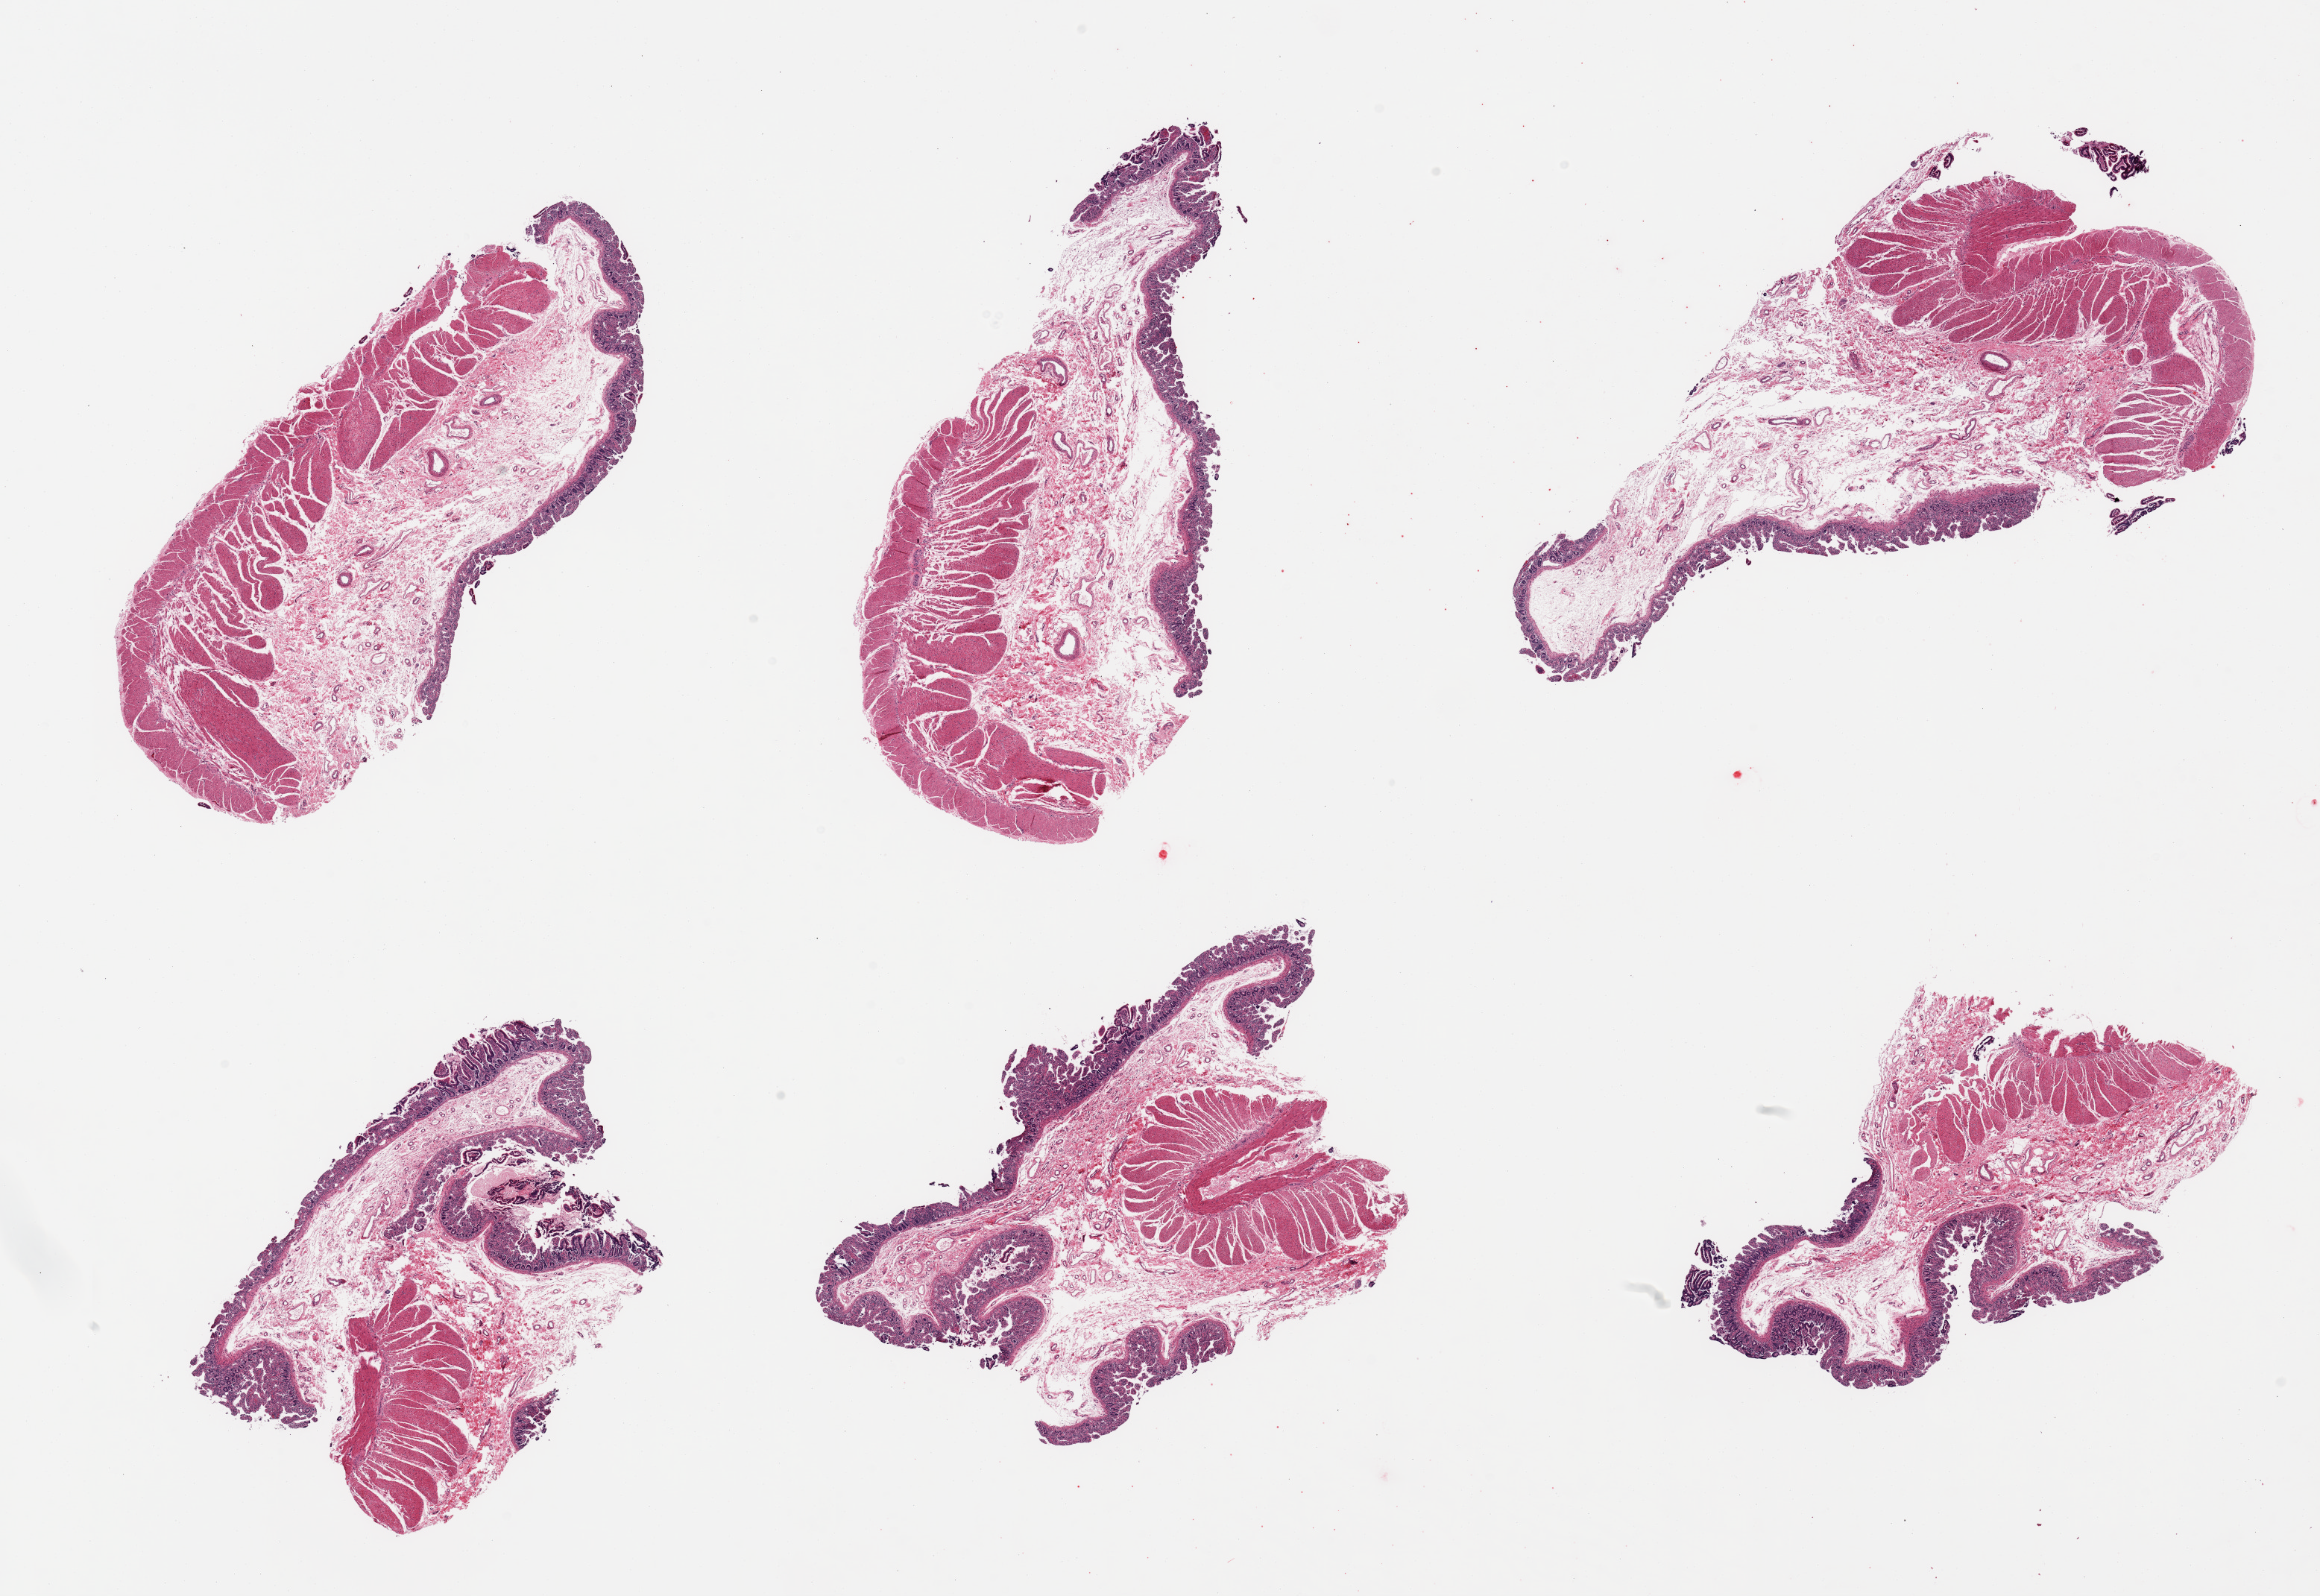
Whole-slide image, haematoxylin and eosin stain, brightfield — a low-resolution overview of the entire scanned area, about 24.6 x 16.9 mm; PAXgene-fixed, paraffin-embedded tissue; sampled site (target tissue): transverse colon; tissue donor sample. Male donor.
Review note (as recorded): 6 pieces; full thickness sections, small intestine.